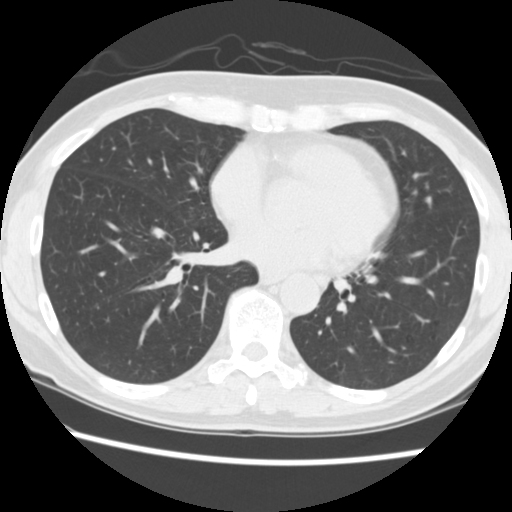
Chest CT (low-dose screening protocol), one axial image. Second annual screen. Lung window (W 1500 / L -600 HU). 120 kVp. Slice 146 of 258 in the series. 512 × 512 image matrix, field of view 330 × 330 mm. Female participant, aged 60 years at enrolment.
Expert-annotated lung lesion, box from (x=412, y=186) to (x=447, y=221) px. No non-calcified nodule or mass ≥4 mm was recorded by the screening reader at this exam. Official screen result: negative screen, minor abnormalities not suspicious for lung cancer. Later outcome: lung cancer diagnosed 509 days after this screen — adenocarcinoma, NOS, lingula, poorly differentiated (G3), stage IA (AJCC 6th edition), 6 mm at pathology.